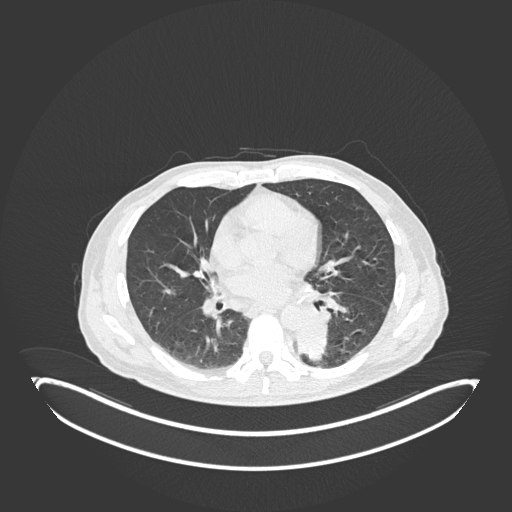
Chest CT, one axial slice. Slice 91 of 251 in the series (ordered by position). Lung window (W 1500 / L -600 HU). 1 mm slice thickness. 512 × 512 image matrix, field of view 500 × 500 mm. Patient: male, 72 years. From the clinical record (not read from this slice): clinical TNM (as recorded): T2b N0 M1.
Annotated regions visible in this slice (rectangle marked by the reading radiologist):
- lung tumour (recorded histology: adenocarcinoma): bounding box (x1, y1, x2, y2) in pixels: (291, 321, 331, 364)